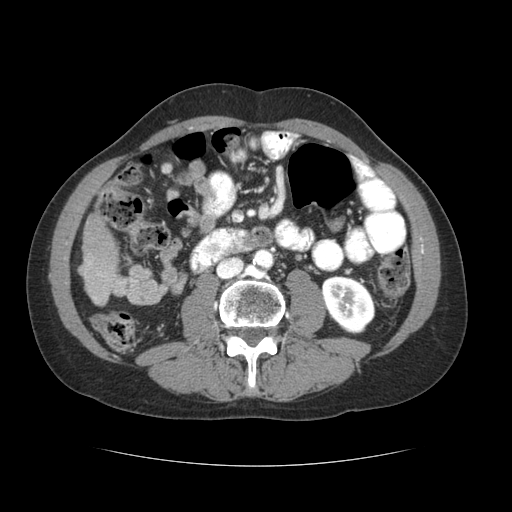
Contrast-enhanced abdominal CT (liver protocol), one axial slice. Slice 8 of 69 in the series (ordered by position). Reconstruction kernel STANDARD. 120 kVp. Soft-tissue window (W 400 / L 40 HU). 512 × 512 image matrix, field of view 360 × 360 mm. Case-level facts recorded for this patient, not image findings: diagnosis: hepatocellular carcinoma (patient treated with transarterial chemoembolisation; whether this scan precedes or follows treatment is not stated here); TNM stage (as recorded): Stage-II.
Annotated regions visible in this slice (semi-automatically segmented with operator editing):
- liver parenchyma outside the tumour (the mass and vessels are separate outlines, so this box may not span the whole liver): bounding box <80,212,118,290> (left, top, right, bottom; pixels)
- liver vessels: <88,261,102,276>